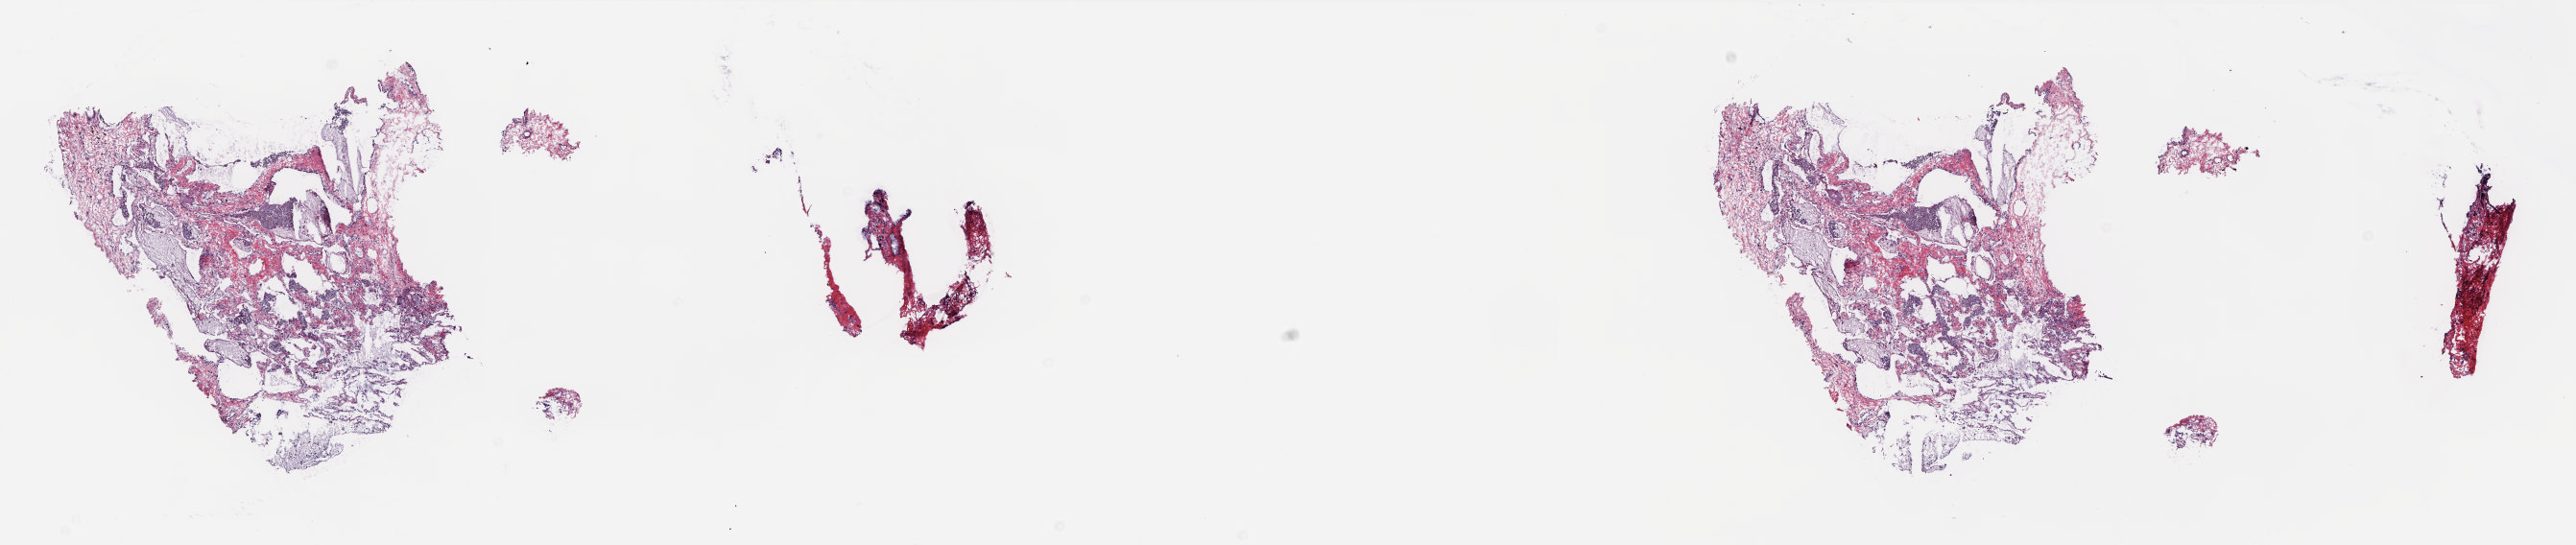
Digitized H&E tissue section (whole slide), a low-resolution overview of the entire scanned area, about 21.6 x 4.6 mm. Frozen section. Sample: solid tissue normal (non-tumour tissue), lung. Male patient; age at initial diagnosis 43 years. Composition of this section per pathologist review: tumour cells 0%, tumour nuclei 0%, normal cells 100%, stromal cells 0%, necrosis 0%. Infiltration values recorded for this section: lymphocyte infiltration 4%, monocyte infiltration 10%, neutrophil infiltration 0%.
This section: solid tissue normal (non-tumour) sample from the same patient. Patient diagnosis: Adenocarcinoma, NOS (upper lobe, lung).